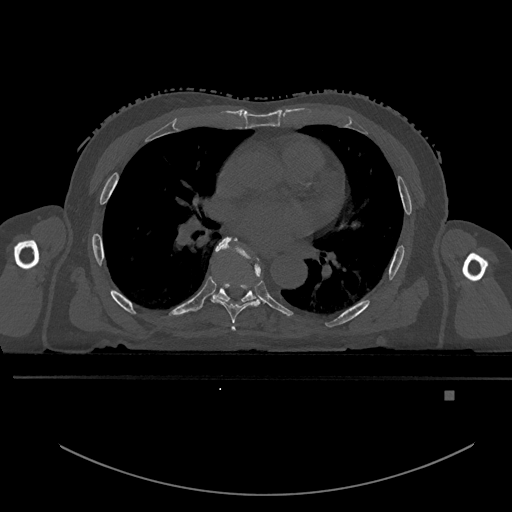
CT including the spine, one axial slice; slice 284 of 969 in the series (ordered by position); bone window (W 1800 / L 400 HU); 0.5 mm slice thickness; 512 × 512 image matrix, field of view 456 × 456 mm. Patient: male, 82 years. From the clinical record (not read from this slice): primary cancer: prostate; vertebrae with lytic lesions (as recorded): T11, T9, T8, T2.
Structures marked on this image (semi-automatic segmentation, software-assisted and operator-edited):
- T5 vertebra: box from (x=231, y=326) to (x=235, y=331) px
- T6 vertebra: (x=211, y=236)–(x=261, y=324)
- T7 vertebra: (x=214, y=284)–(x=256, y=302)